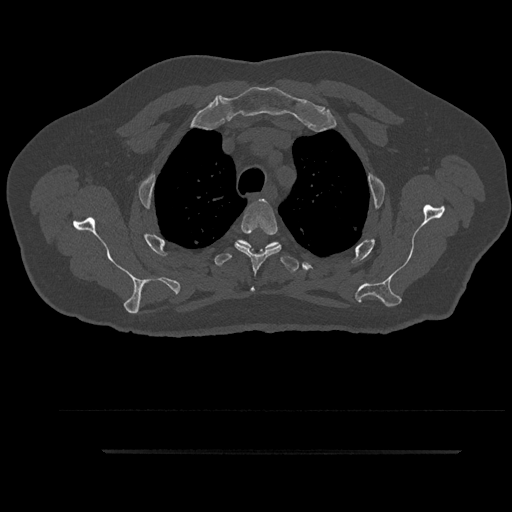
CT including the spine, one axial slice. Slice 706 of 797 in the series (ordered by position). 120 kVp. Bone window (W 1800 / L 400 HU). 512 × 512 image matrix. Male patient, age 63 years. Case-level facts recorded for this patient, not image findings: primary cancer: renal; vertebrae with lytic lesions (as recorded): T8.
Annotated regions visible in this slice (semi-automatically segmented with operator editing):
- T3 vertebra: bounding box (x1, y1, x2, y2) in pixels: (235, 199, 281, 291)
- T4 vertebra: (214, 240, 299, 272)